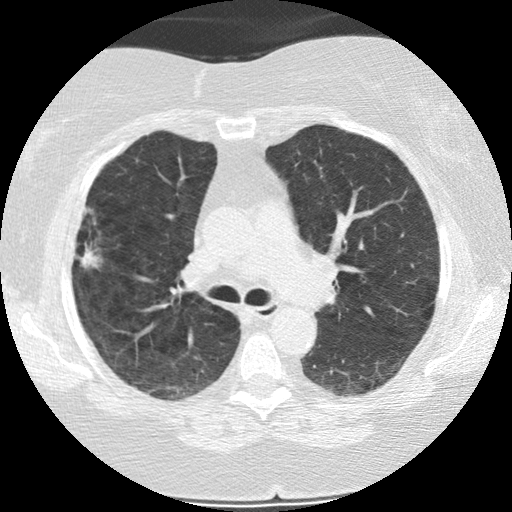
Chest CT (low-dose screening protocol), one axial image. Baseline annual screen. Lung window (W 1500 / L -600 HU). 2.5 mm slice thickness. 120 kVp. Female, age 73 years at enrolment.
Expert-annotated lung lesion, box from (x=59, y=210) to (x=110, y=275) px. Reader record for this screening exam (exam-level; its link to the box is not recorded): non-calcified nodule or mass ≥4 mm, right upper lobe, 21 × 14 mm, poorly defined margins, soft tissue attenuation.